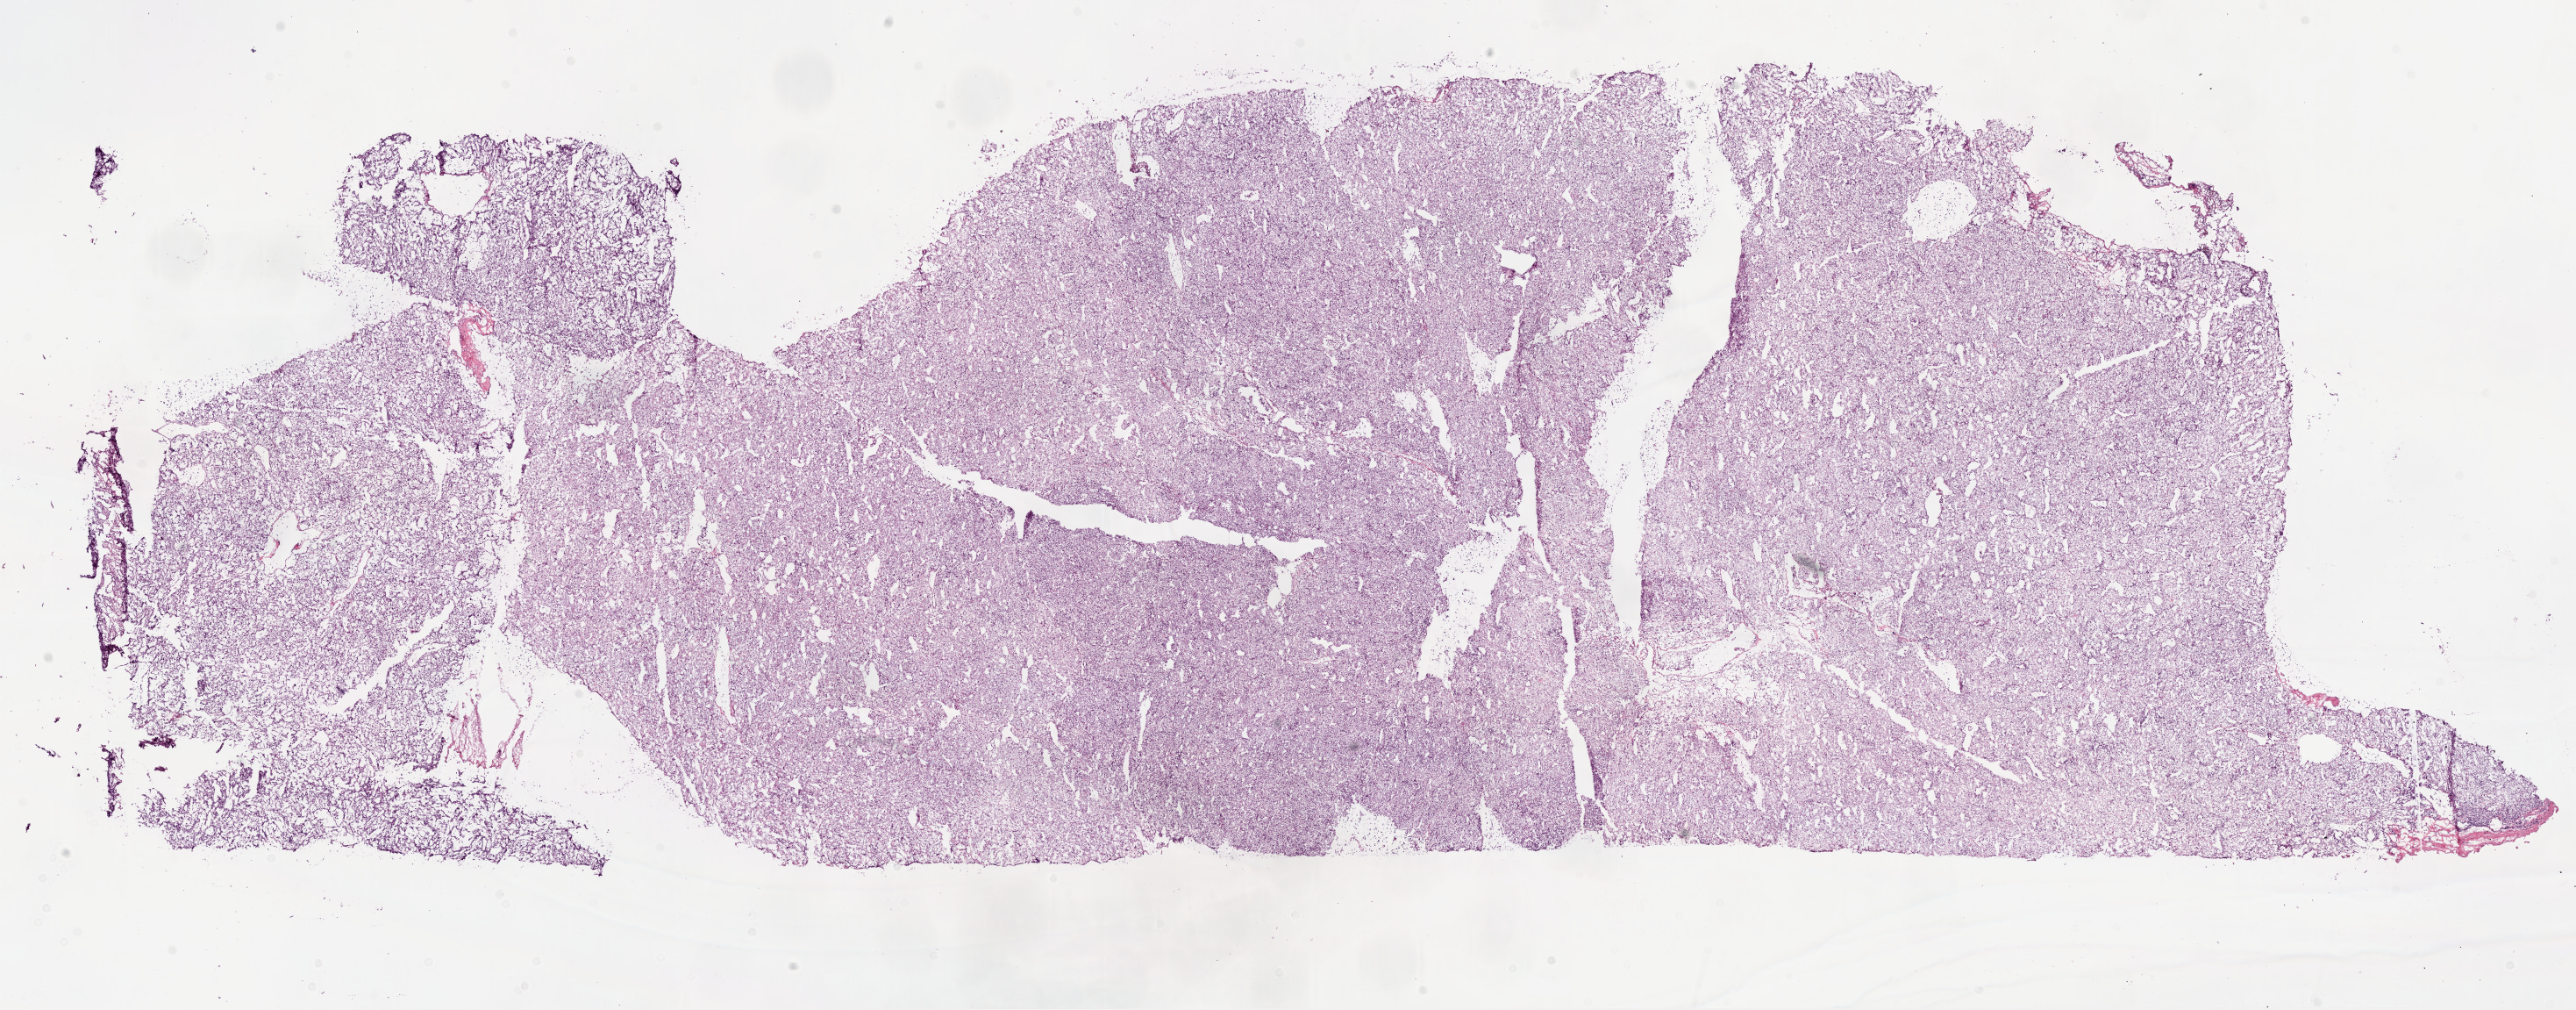
H&E-stained whole-slide image — a low-resolution overview of the entire scanned area, about 23.7 x 9.3 mm (from a 20x scan). Frozen section from the bottom of the tissue portion. Kidney, primary tumour sample. Male patient; age at initial diagnosis 62 years. Histologic grade: G3 (poorly differentiated). Slide review estimates, as recorded: tumour cells 95%, tumour nuclei 85%, normal cells 0%, stromal cells 5%, necrosis 0%.
• laterality: left
• AJCC pathologic stage: IV
• histologic diagnosis: Clear cell adenocarcinoma, NOS
• TNM: T2b N0 M1